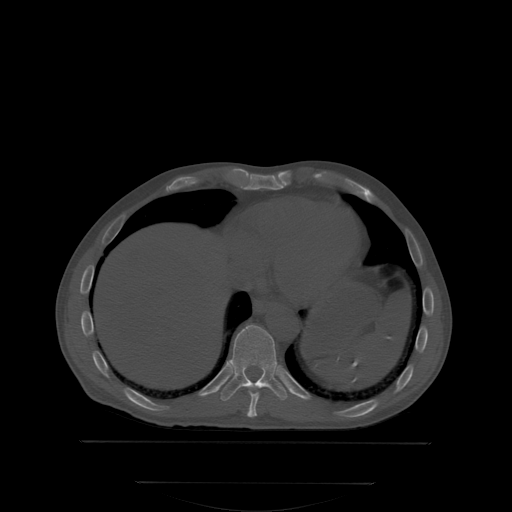
CT including the spine, one axial slice. Position 196 of 350 along the scan axis. Bone window (W 1800 / L 400 HU). 2.5 mm slice thickness. 512 × 512 image matrix, field of view 500 × 500 mm. Male patient, age 58 years. From the clinical record (not read from this slice): primary cancer: prostate; vertebrae with lytic lesions (as recorded): L1.
Annotated regions visible in this slice (semi-automatically segmented with operator editing):
- T10 vertebra: box from (x=221, y=325) to (x=287, y=401) px
- T9 vertebra: (x=247, y=388)–(x=259, y=417)